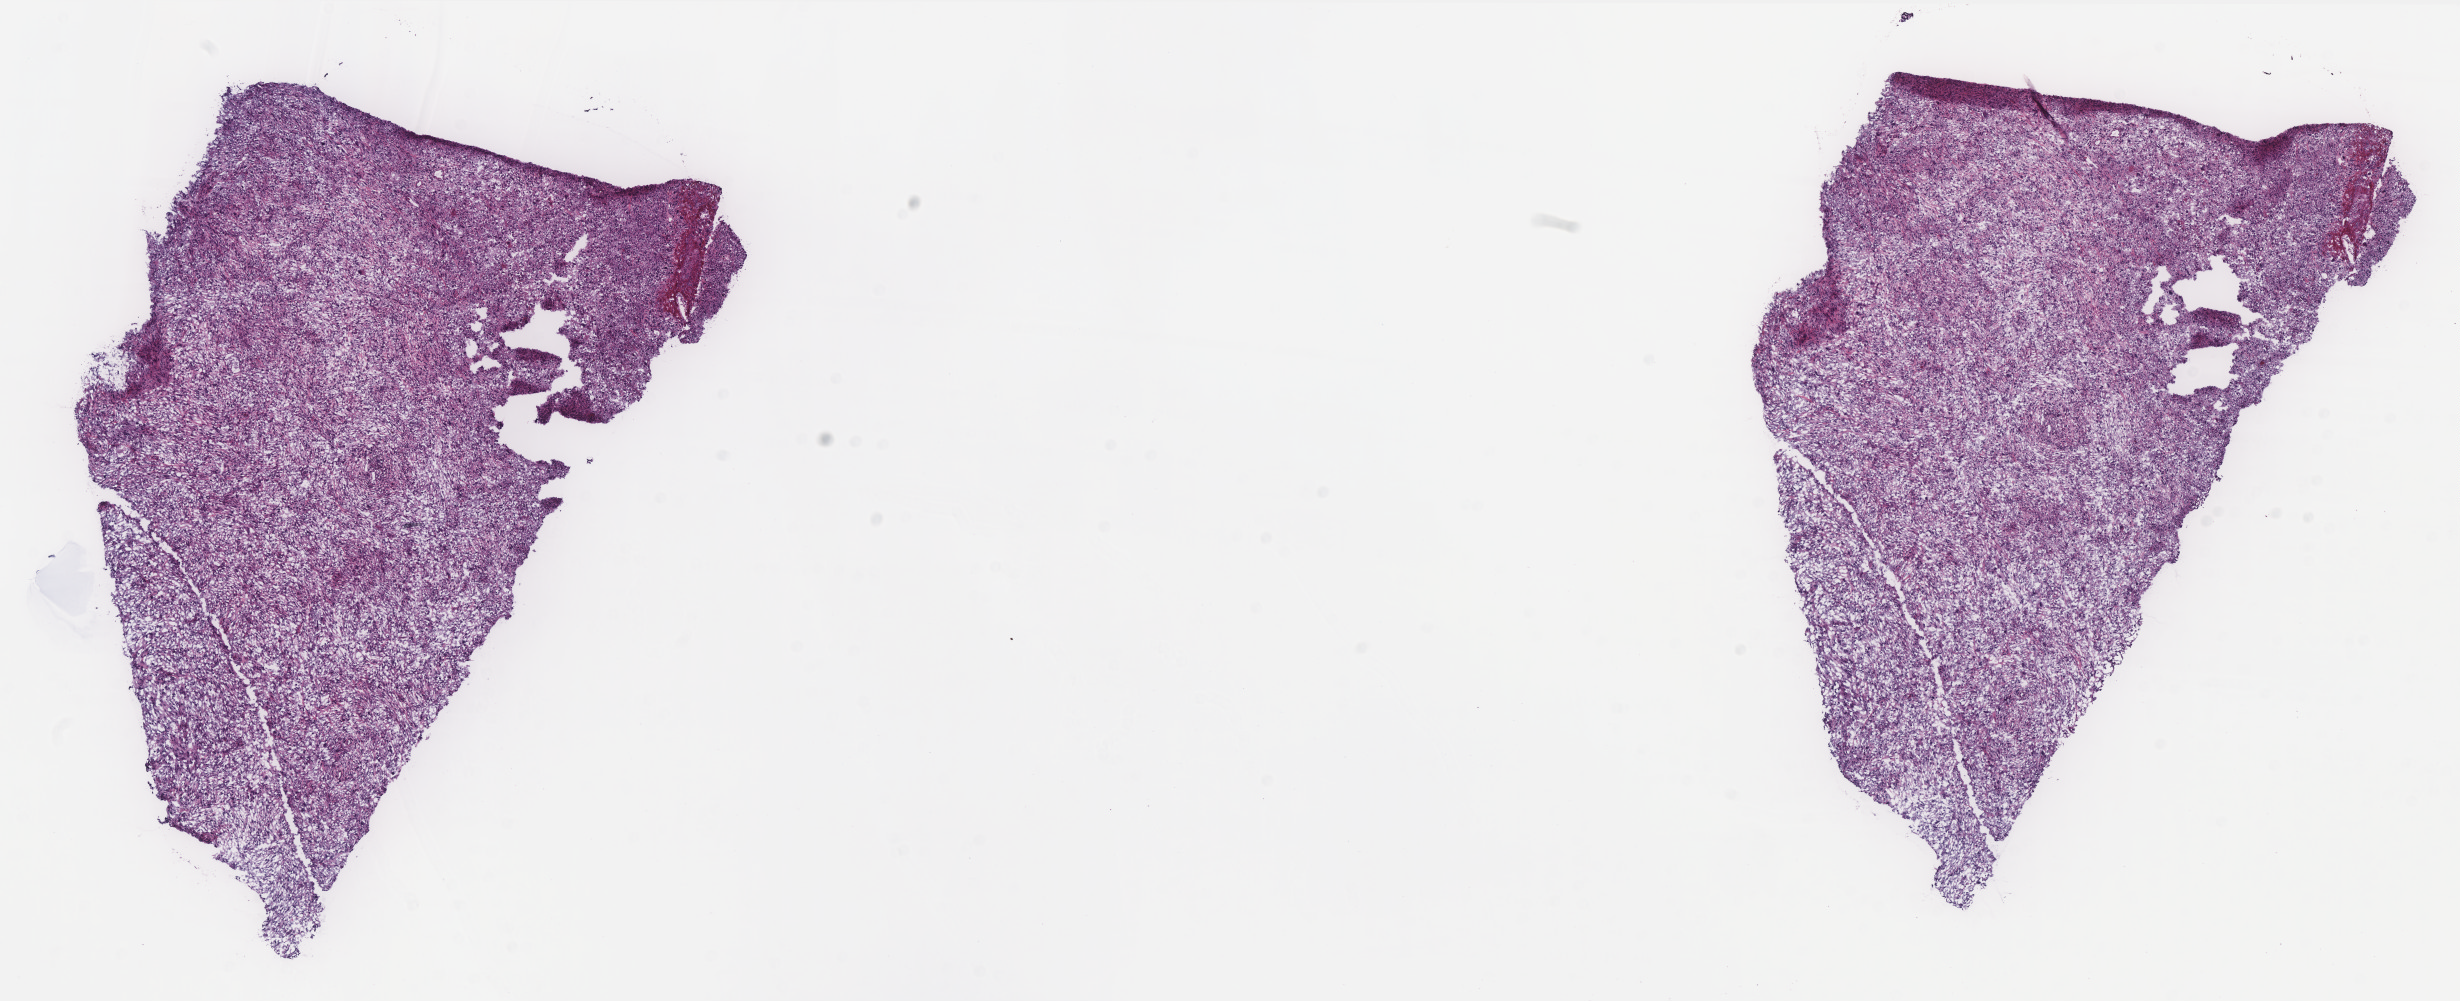
Whole-slide histology image, Hematoxylin and eosin (H&E) stained — low-resolution overview of the scanned area, about 19.7 x 8.0 mm (acquisition: 40x scan), frozen section, primary tumour sample from the retroperitoneum and peritoneum. Patient: male, age at initial diagnosis 66 years. Composition of this section per pathologist review: tumour cells 90%, tumour nuclei 90%, normal cells 0%, stromal cells 10%, necrosis 0%. Infiltration values recorded for this section: lymphocyte infiltration 2%, monocyte infiltration 1%, neutrophil infiltration 1%.
- pathologic diagnosis: Dedifferentiated liposarcoma (retroperitoneum)